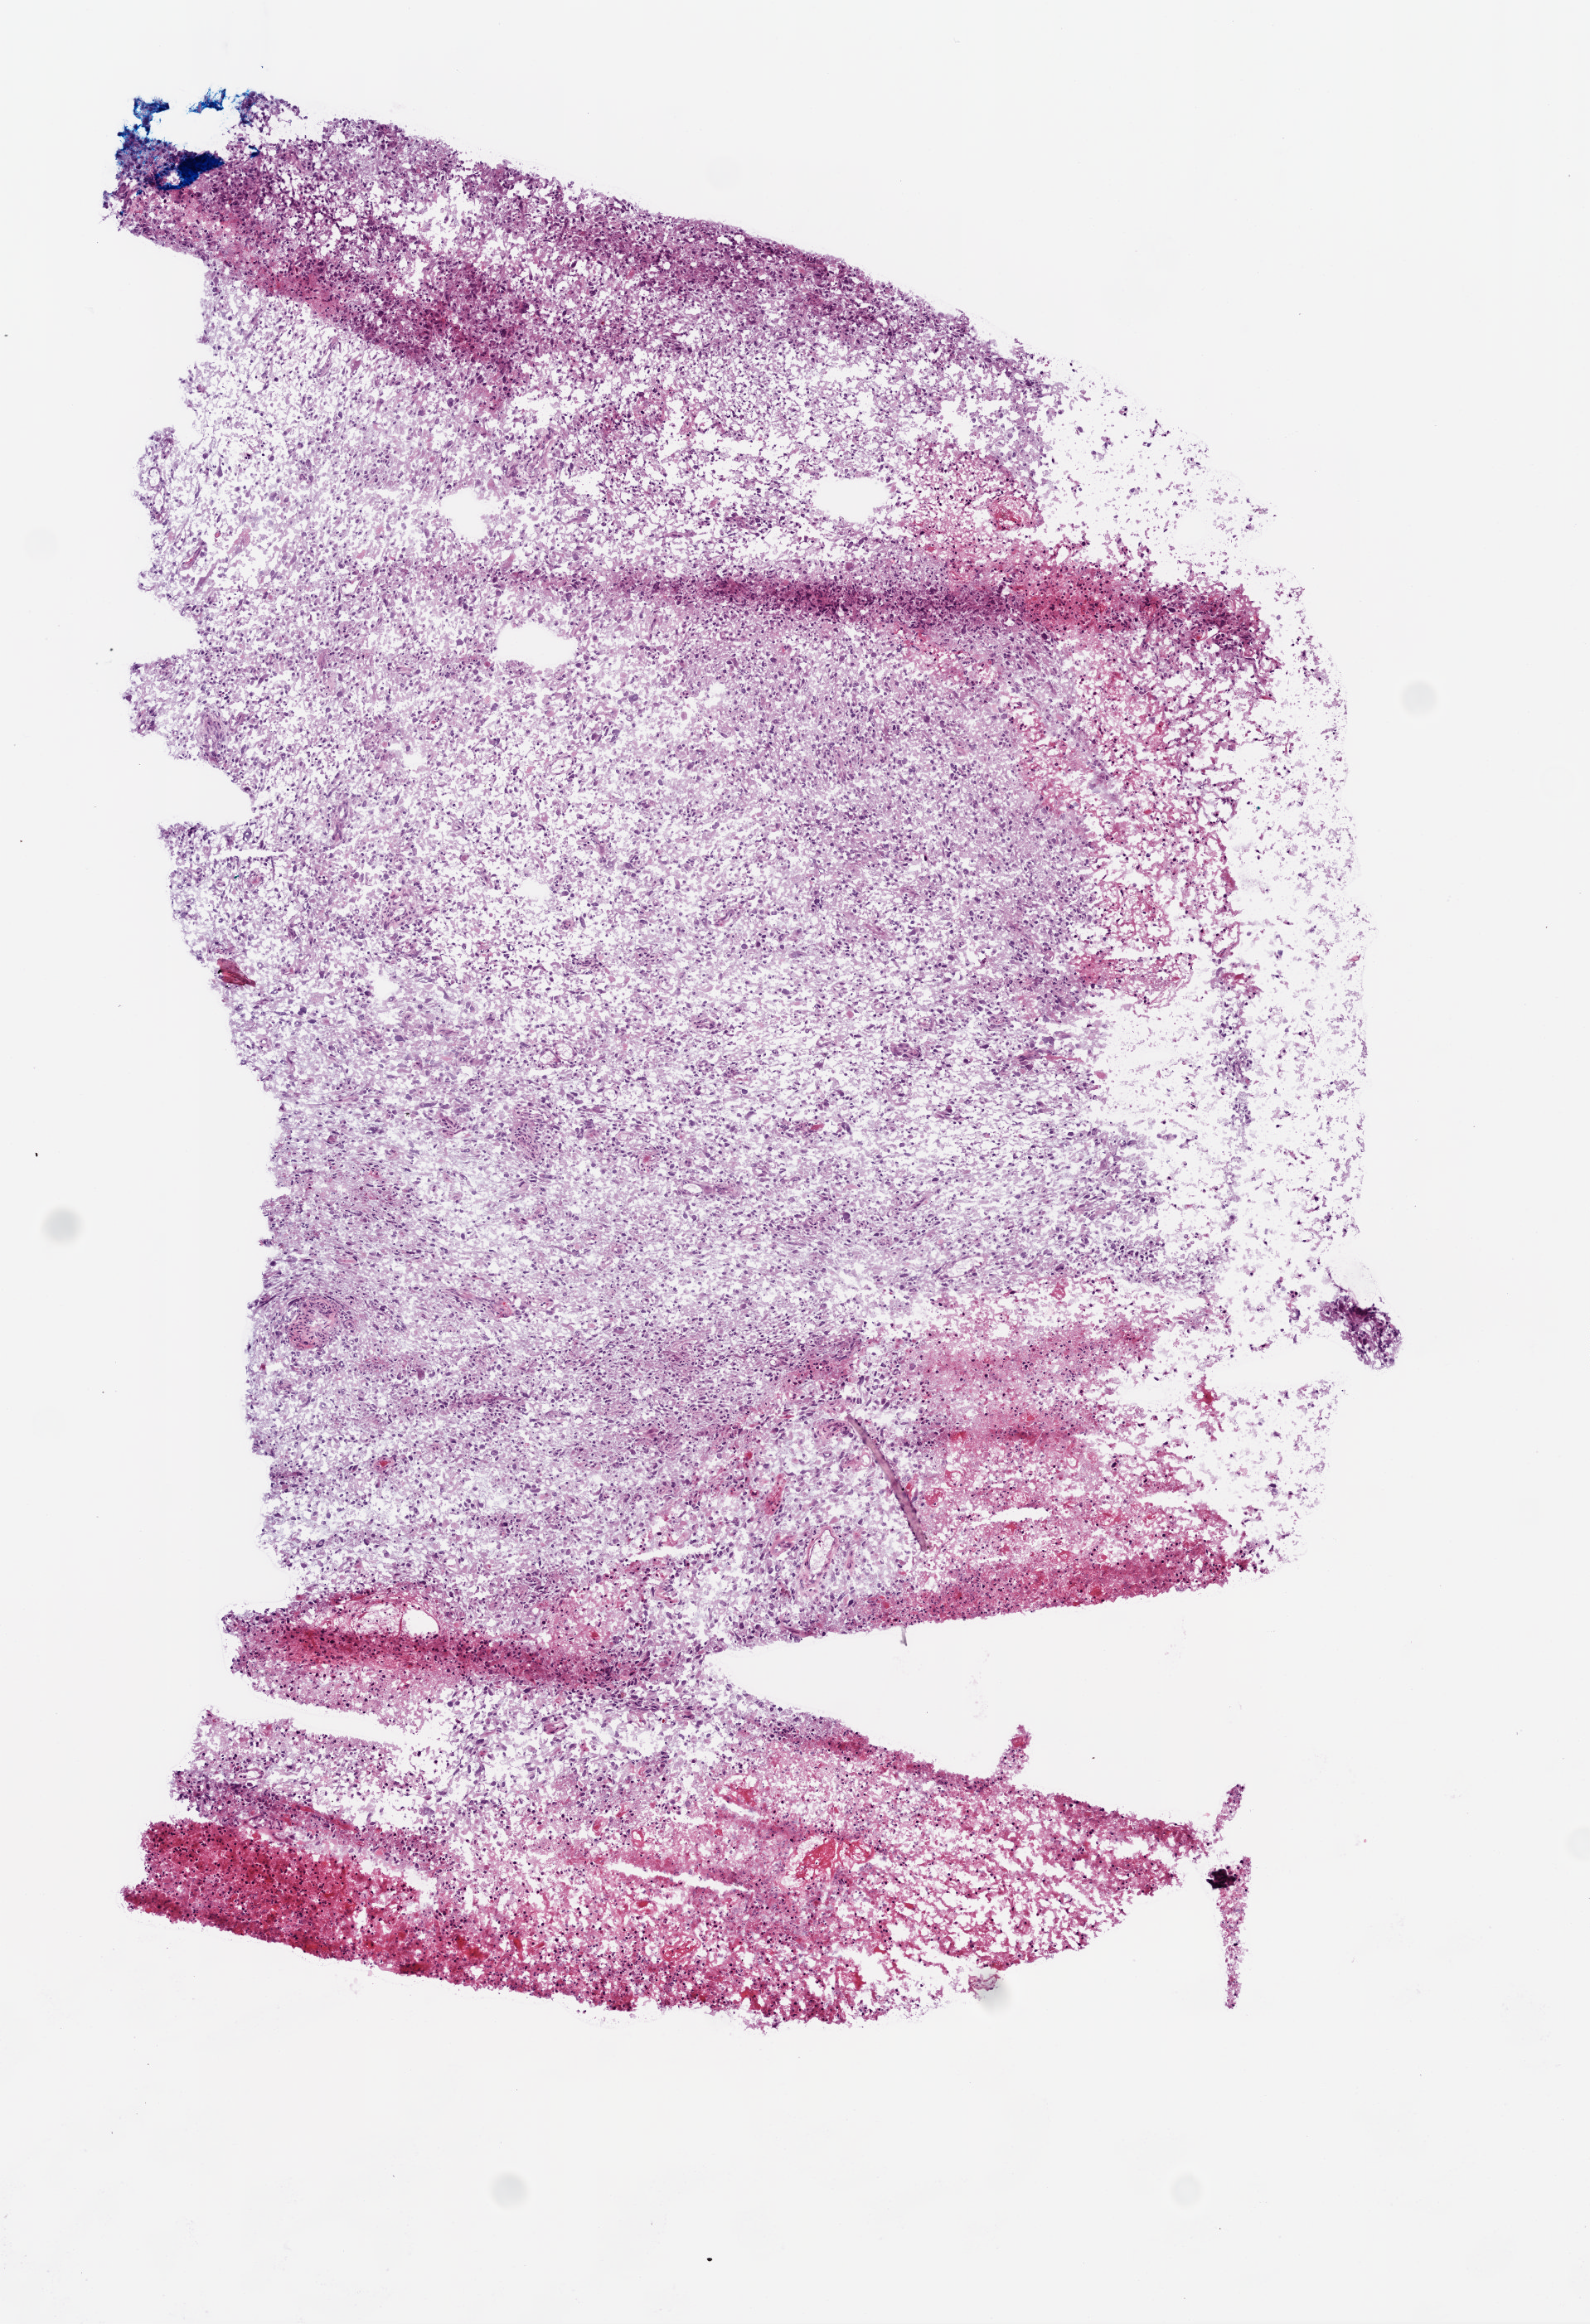
H&E-stained whole-slide image, a low-resolution overview of the entire scanned area, about 3.9 x 5.7 mm (from a 20x scan), frozen section, brain, primary tumour sample. Male, age 58 years at initial diagnosis. Pathologist review of this section (percent, as recorded): tumour cells 75%, tumour nuclei 95%, normal cells 0%, stromal cells 0%, necrosis 25%. Infiltration values recorded for this section: lymphocyte infiltration 100%.
• diagnosis: Glioblastoma